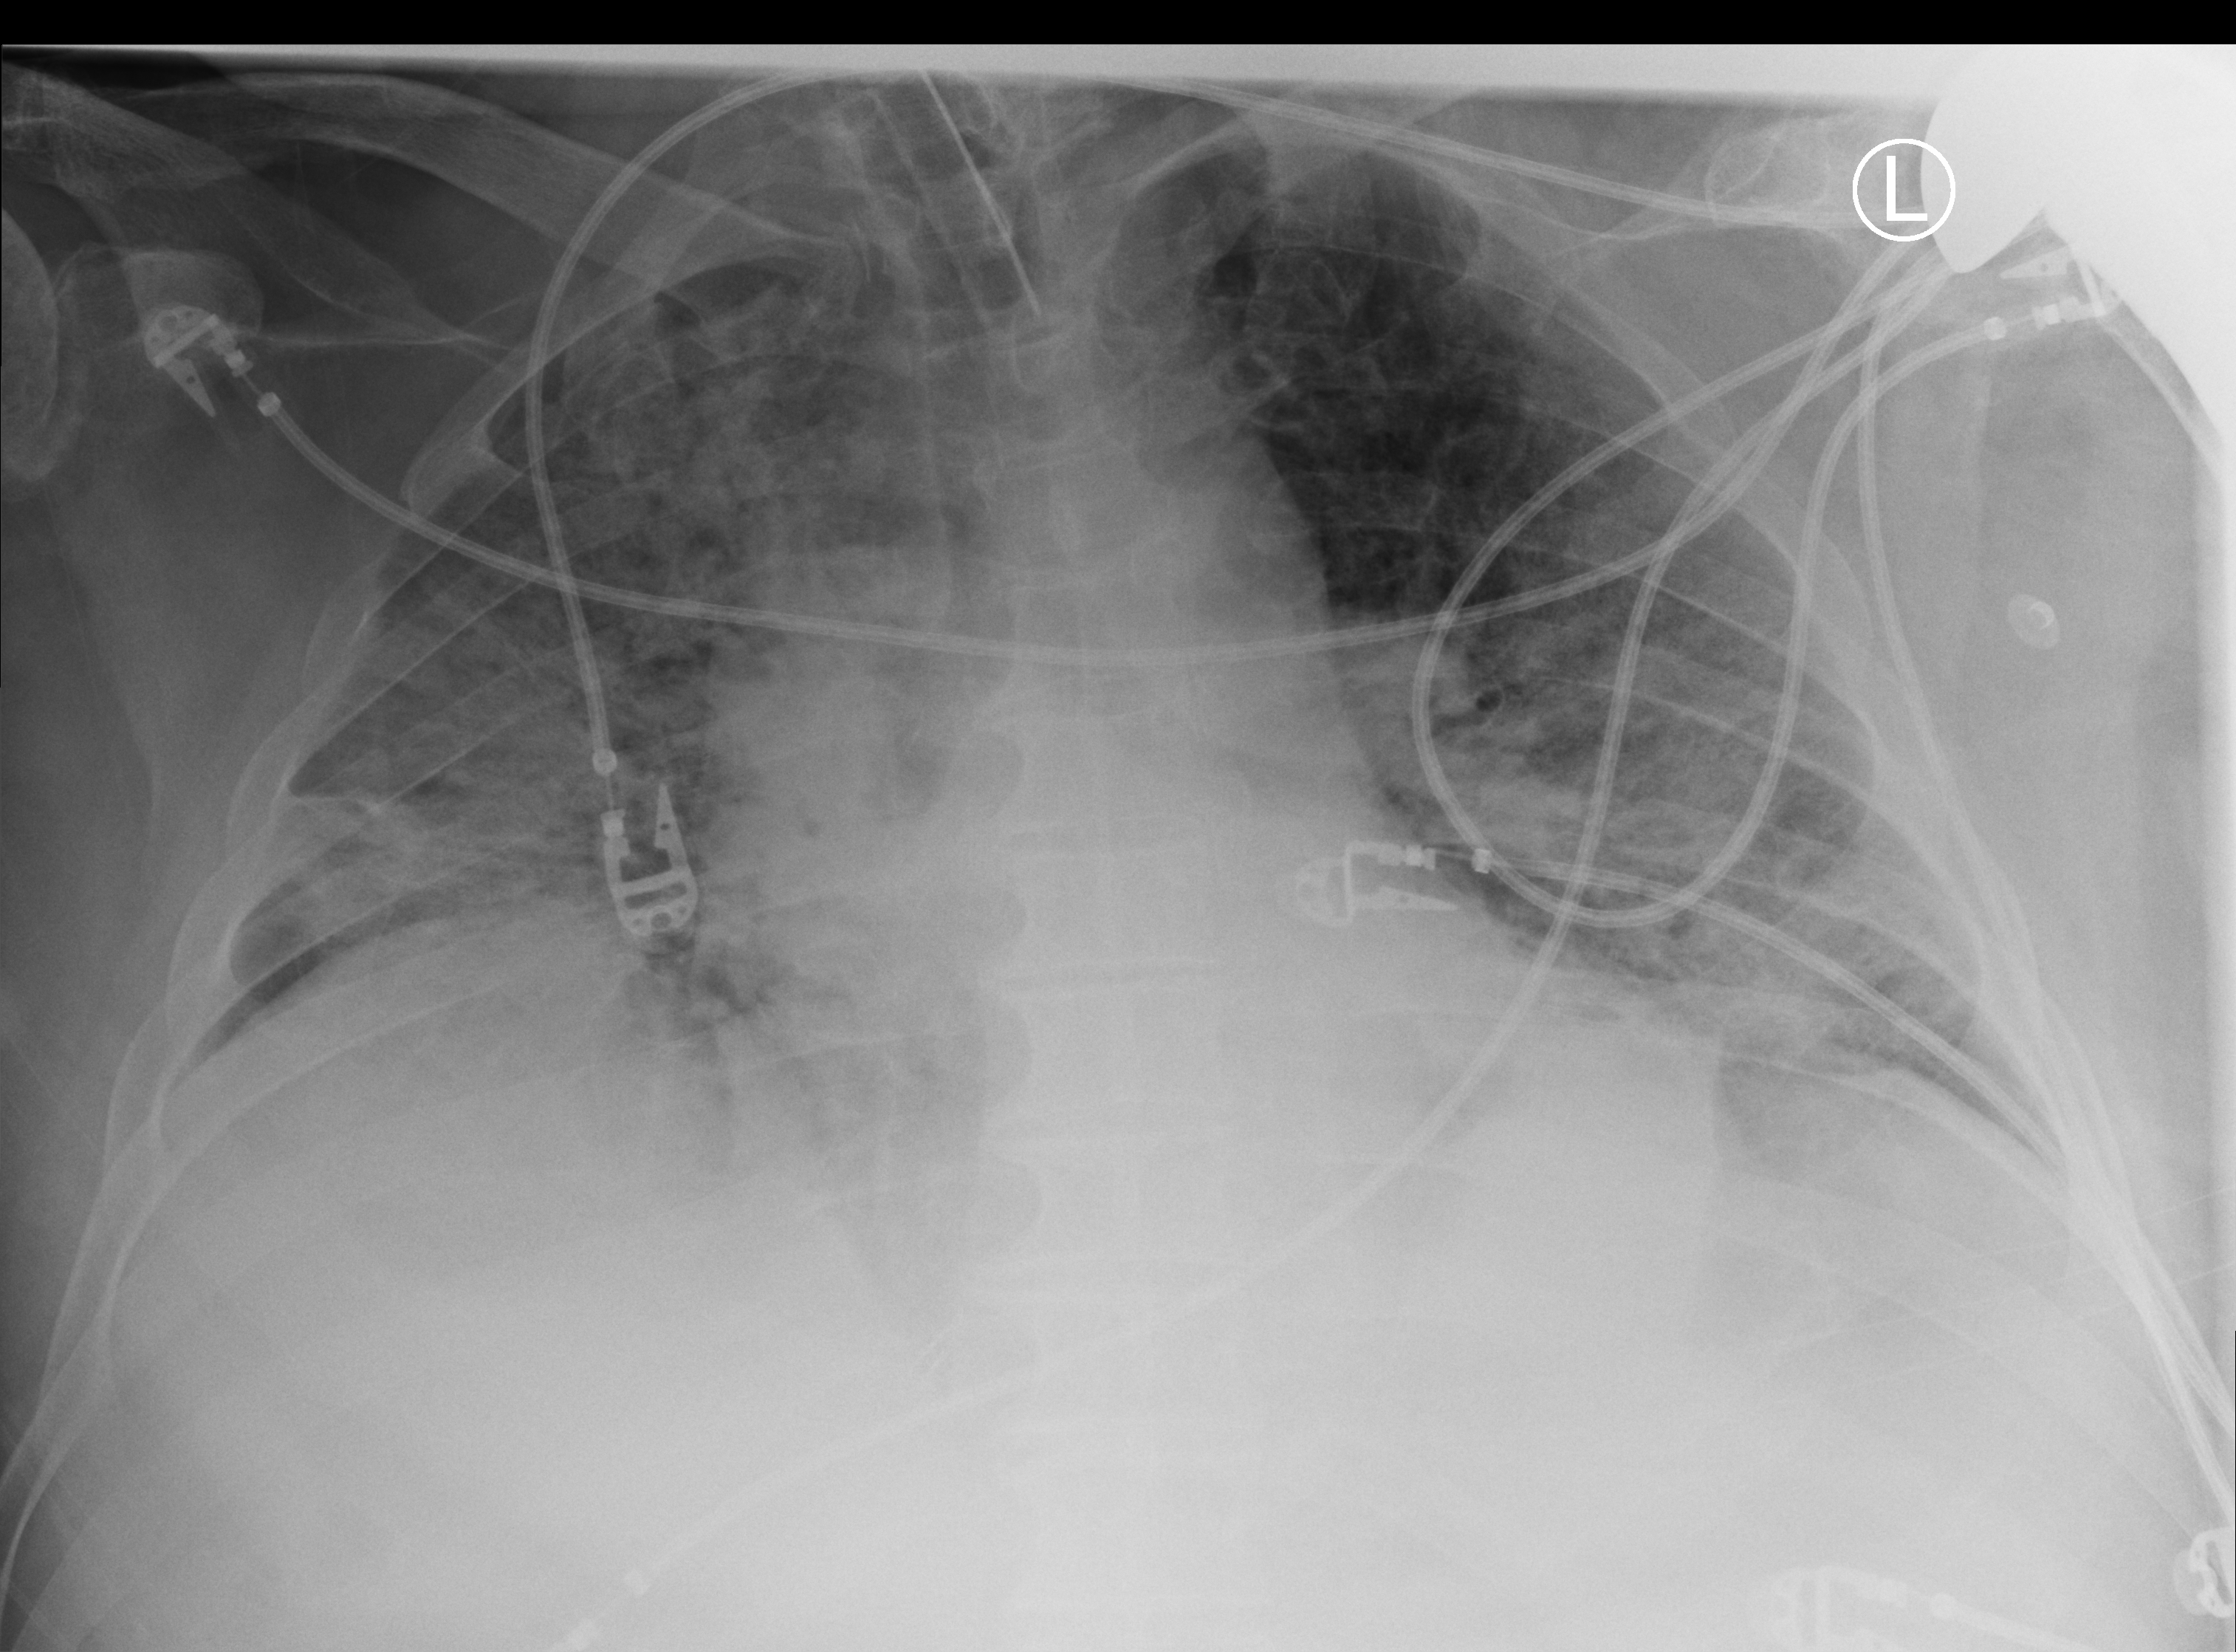
Bedside chest radiograph (computed radiography), anteroposterior (AP) projection. Male patient hospitalised with COVID-19, age 60–74 years.
Admission-level facts for this patient (not findings on this image; timing relative to this image not recorded): length of hospital stay: 10 days; hypertension (admission record): yes.